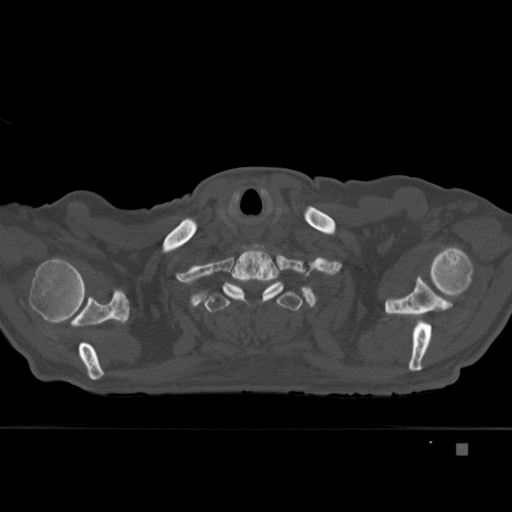
CT including the spine, one axial slice; slice 355 of 451 in the series (ordered by position); bone window (W 1800 / L 400 HU); 1.5 mm slice thickness; 512 × 512 image matrix. Patient: male, 75 years. From the clinical record (not read from this slice): primary cancer: prostate.
Outlined on this slice (semi-automatically segmented with operator editing):
- T1 vertebra: bounding box <222,244,284,305> (left, top, right, bottom; pixels)
- T2 vertebra: <202,284,303,313>